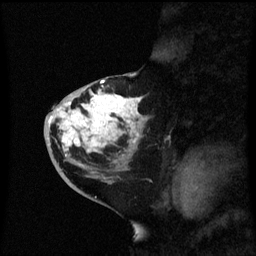
Breast MRI (dynamic contrast-enhanced), one sagittal slice; position 29 of 60 along the scan axis; dynamic contrast-enhanced series, image 2 of 3 at this slice position (ordered by acquisition); 1.5 T; TE 4.2 ms, TR 8.4 ms; 256 × 256 image matrix, field of view 200 × 200 mm. Female patient, age 46 years. Case-level facts recorded for this patient, not image findings: setting: breast cancer imaged before/during neoadjuvant chemotherapy; receptor status: HER2-positive.
Structures marked on this image (semi-automatically segmented with operator editing):
- analysis volume of interest (the breast-tissue region the enhancement analysis was run in; not a lesion): box from (x=44, y=86) to (x=153, y=171) px
- tumour enhancement mask (voxels above the 70 % enhancement threshold inside the analysis volume of interest): (x=50, y=90)–(x=143, y=153)